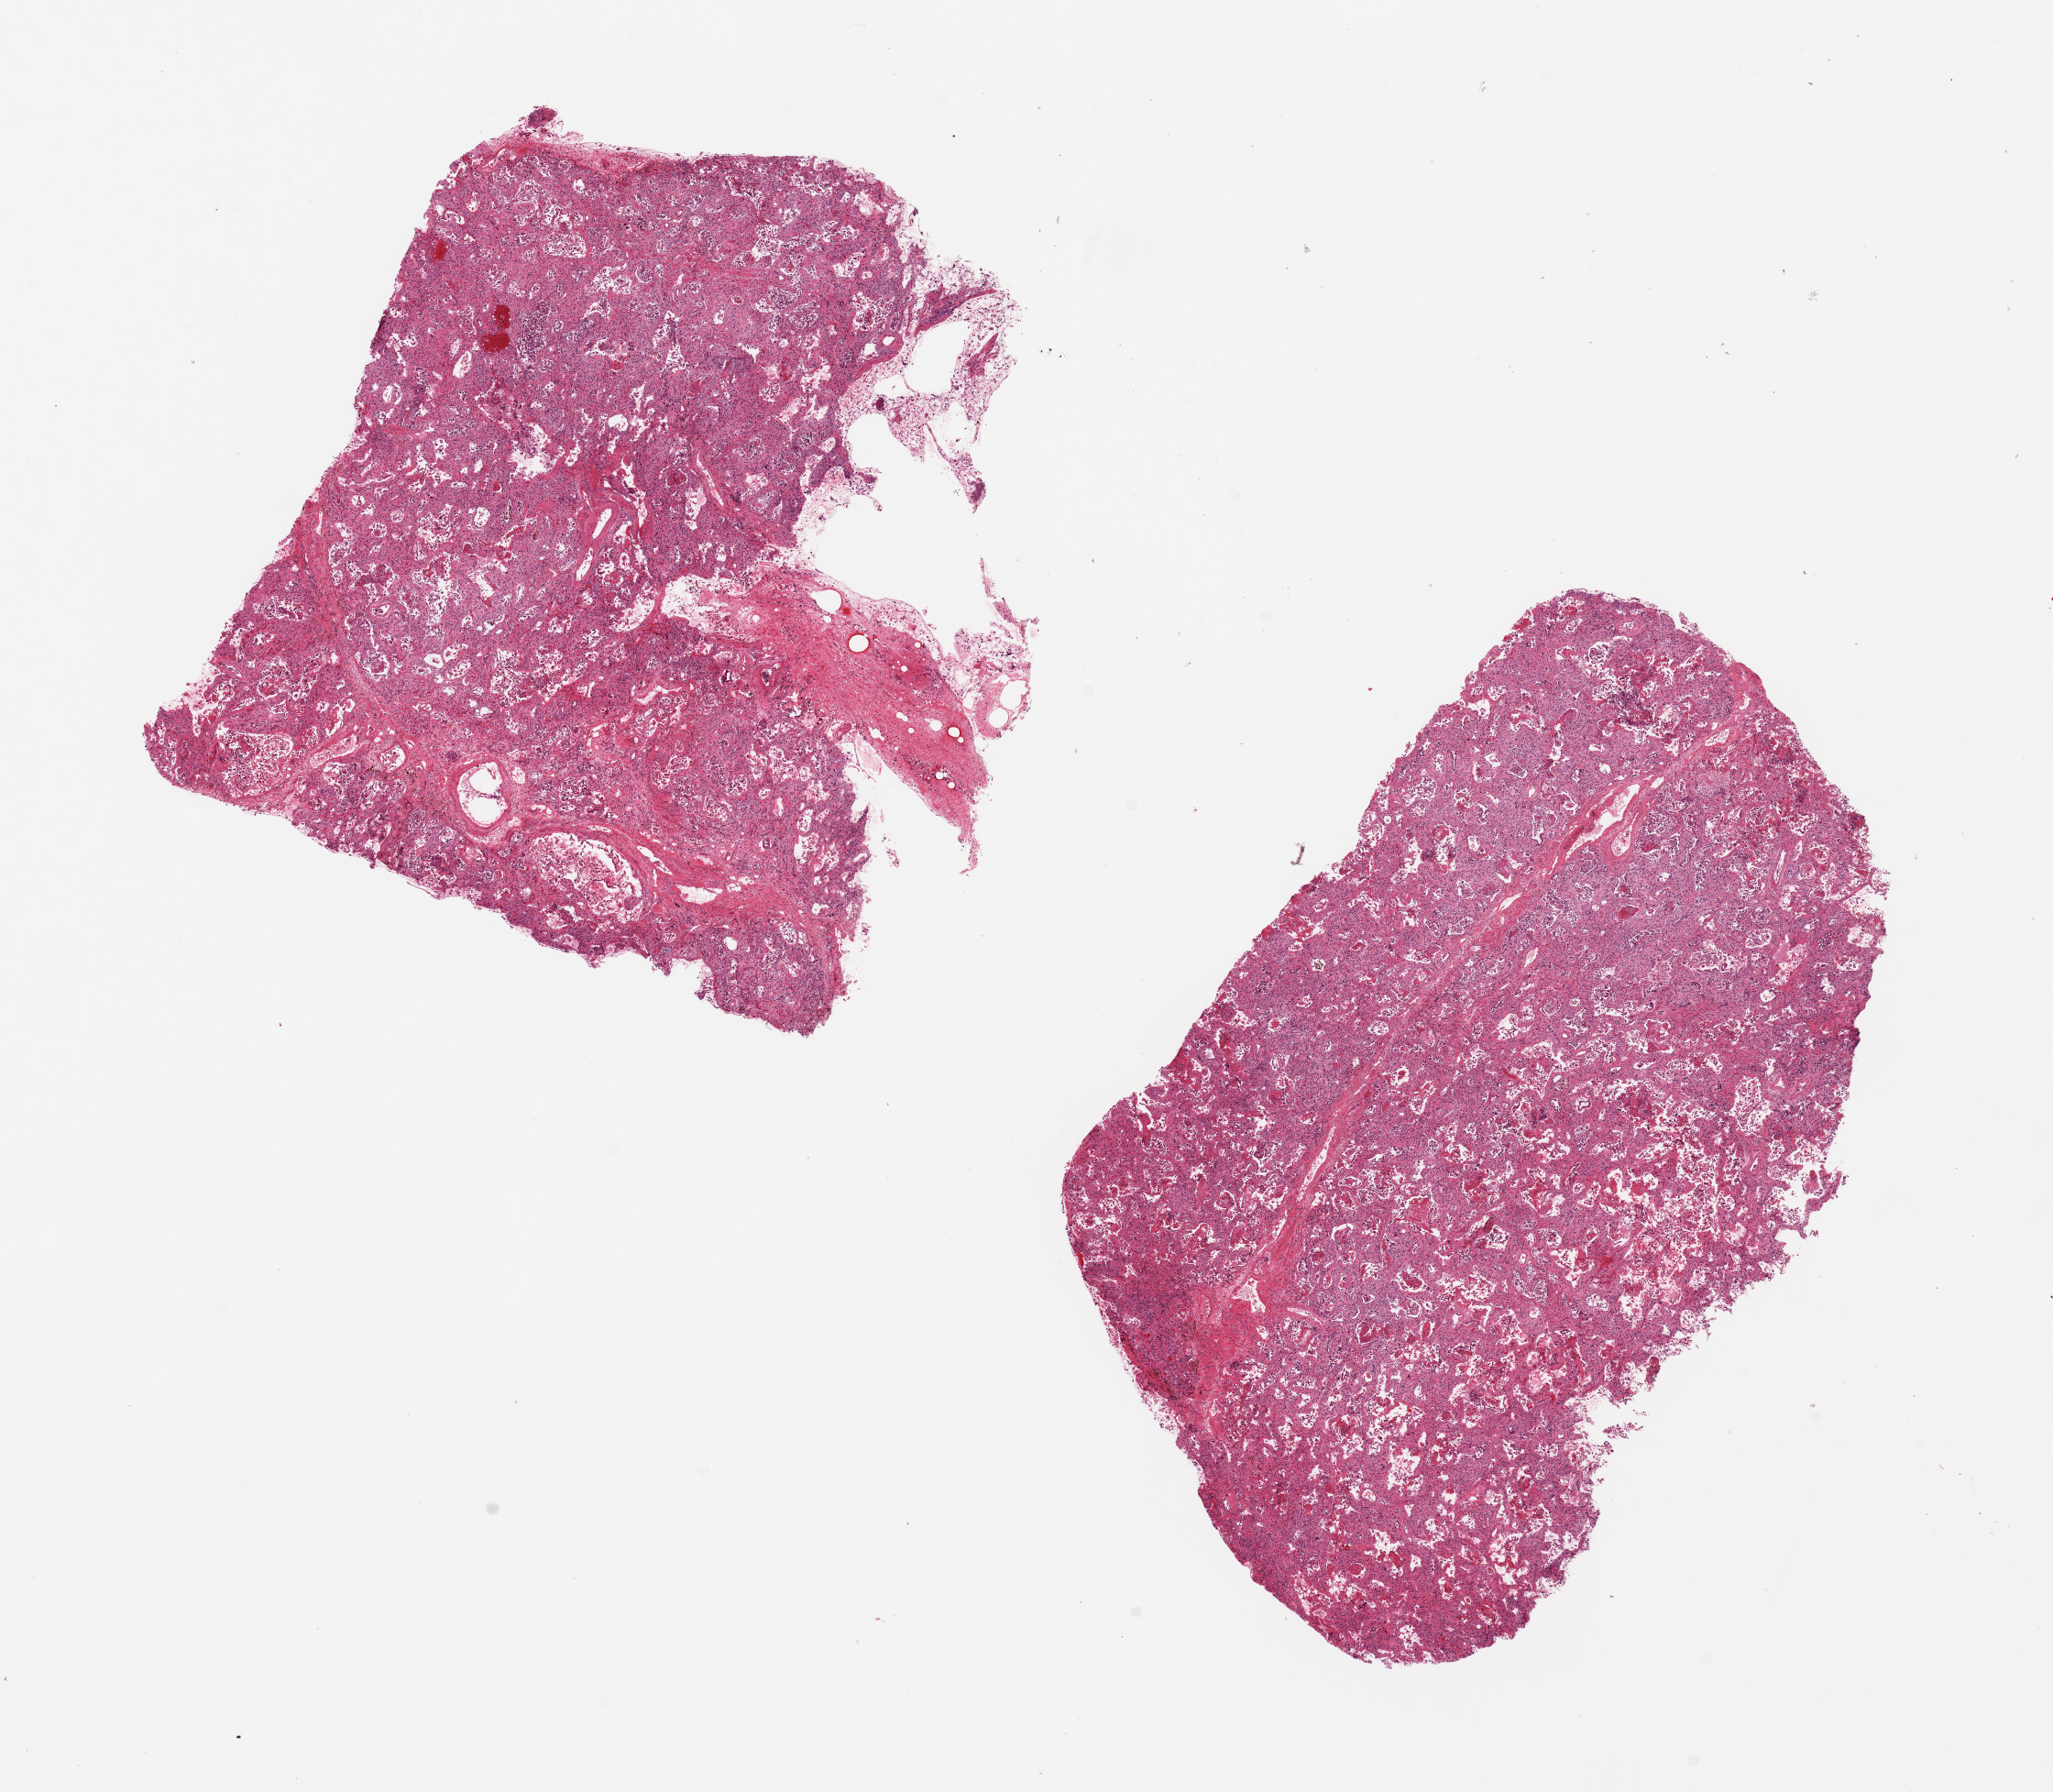
Digitized haematoxylin and eosin-stained section, brightfield, low-resolution overview of the scanned area, about 17.7 x 15.5 mm. PAXgene-fixed, paraffin-embedded tissue. Section of lung (target tissue). Tissue donor sample. Donor sex: male.
Review note (as recorded): 2 pieces, 7x7 & 8x5.5mm; severe interstitial fibrosis, NO normal lung.